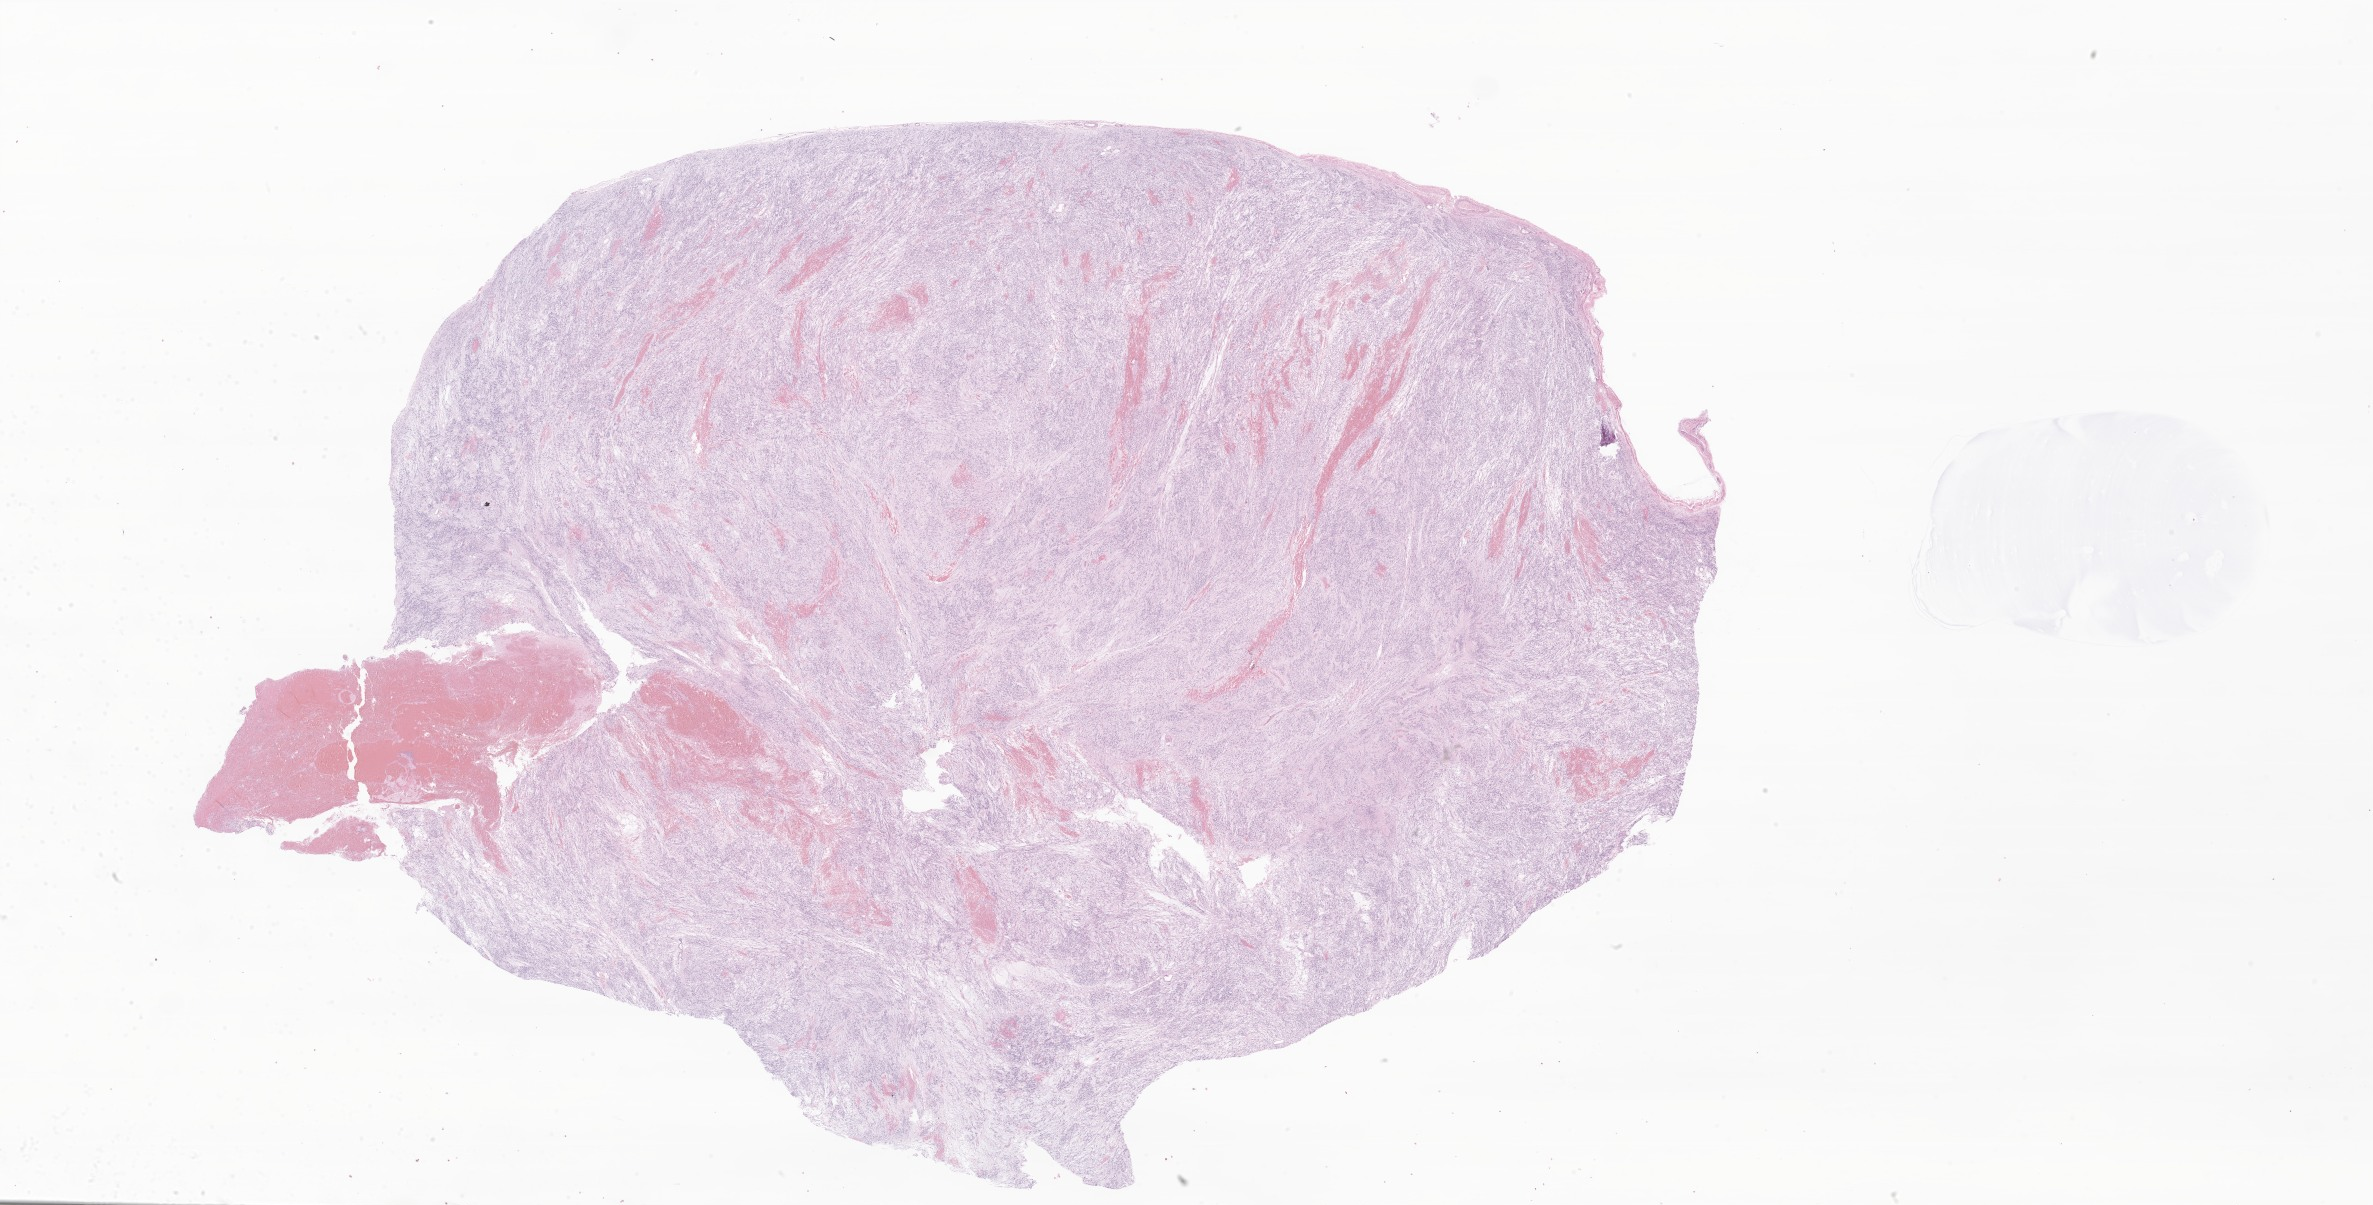
Hematoxylin and eosin (H&E) whole-slide image of tumor tissue from the spinal cord — low-resolution overview of the scanned area, about 40.0 x 20.3 mm. Formalin-fixed, paraffin-embedded (FFPE) tissue. Patient male; age 113 months.
* diagnosis (ICD-O-3 morphology term): Neoplasm, malignant